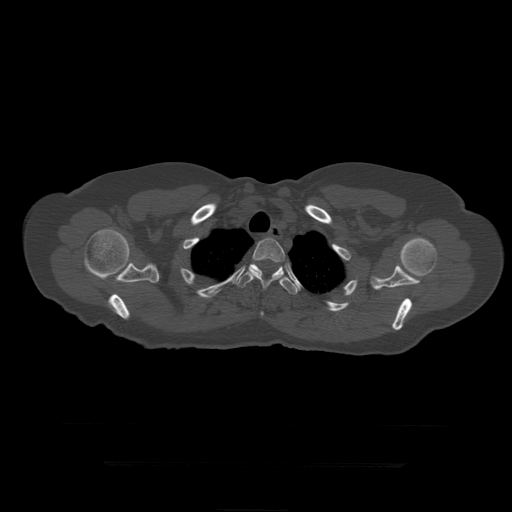
CT including the spine, one axial slice. 120 kVp. Bone window (W 1800 / L 400 HU). 1.25 mm slice thickness. 512 × 512 image matrix. Patient age 41 years. From the clinical record (not read from this slice): primary cancer: breast.
Outlined on this slice (semi-automatically segmented with operator editing):
- T3 vertebra: bounding box <249,238,286,290> (left, top, right, bottom; pixels)
- T4 vertebra: <237,262,299,316>